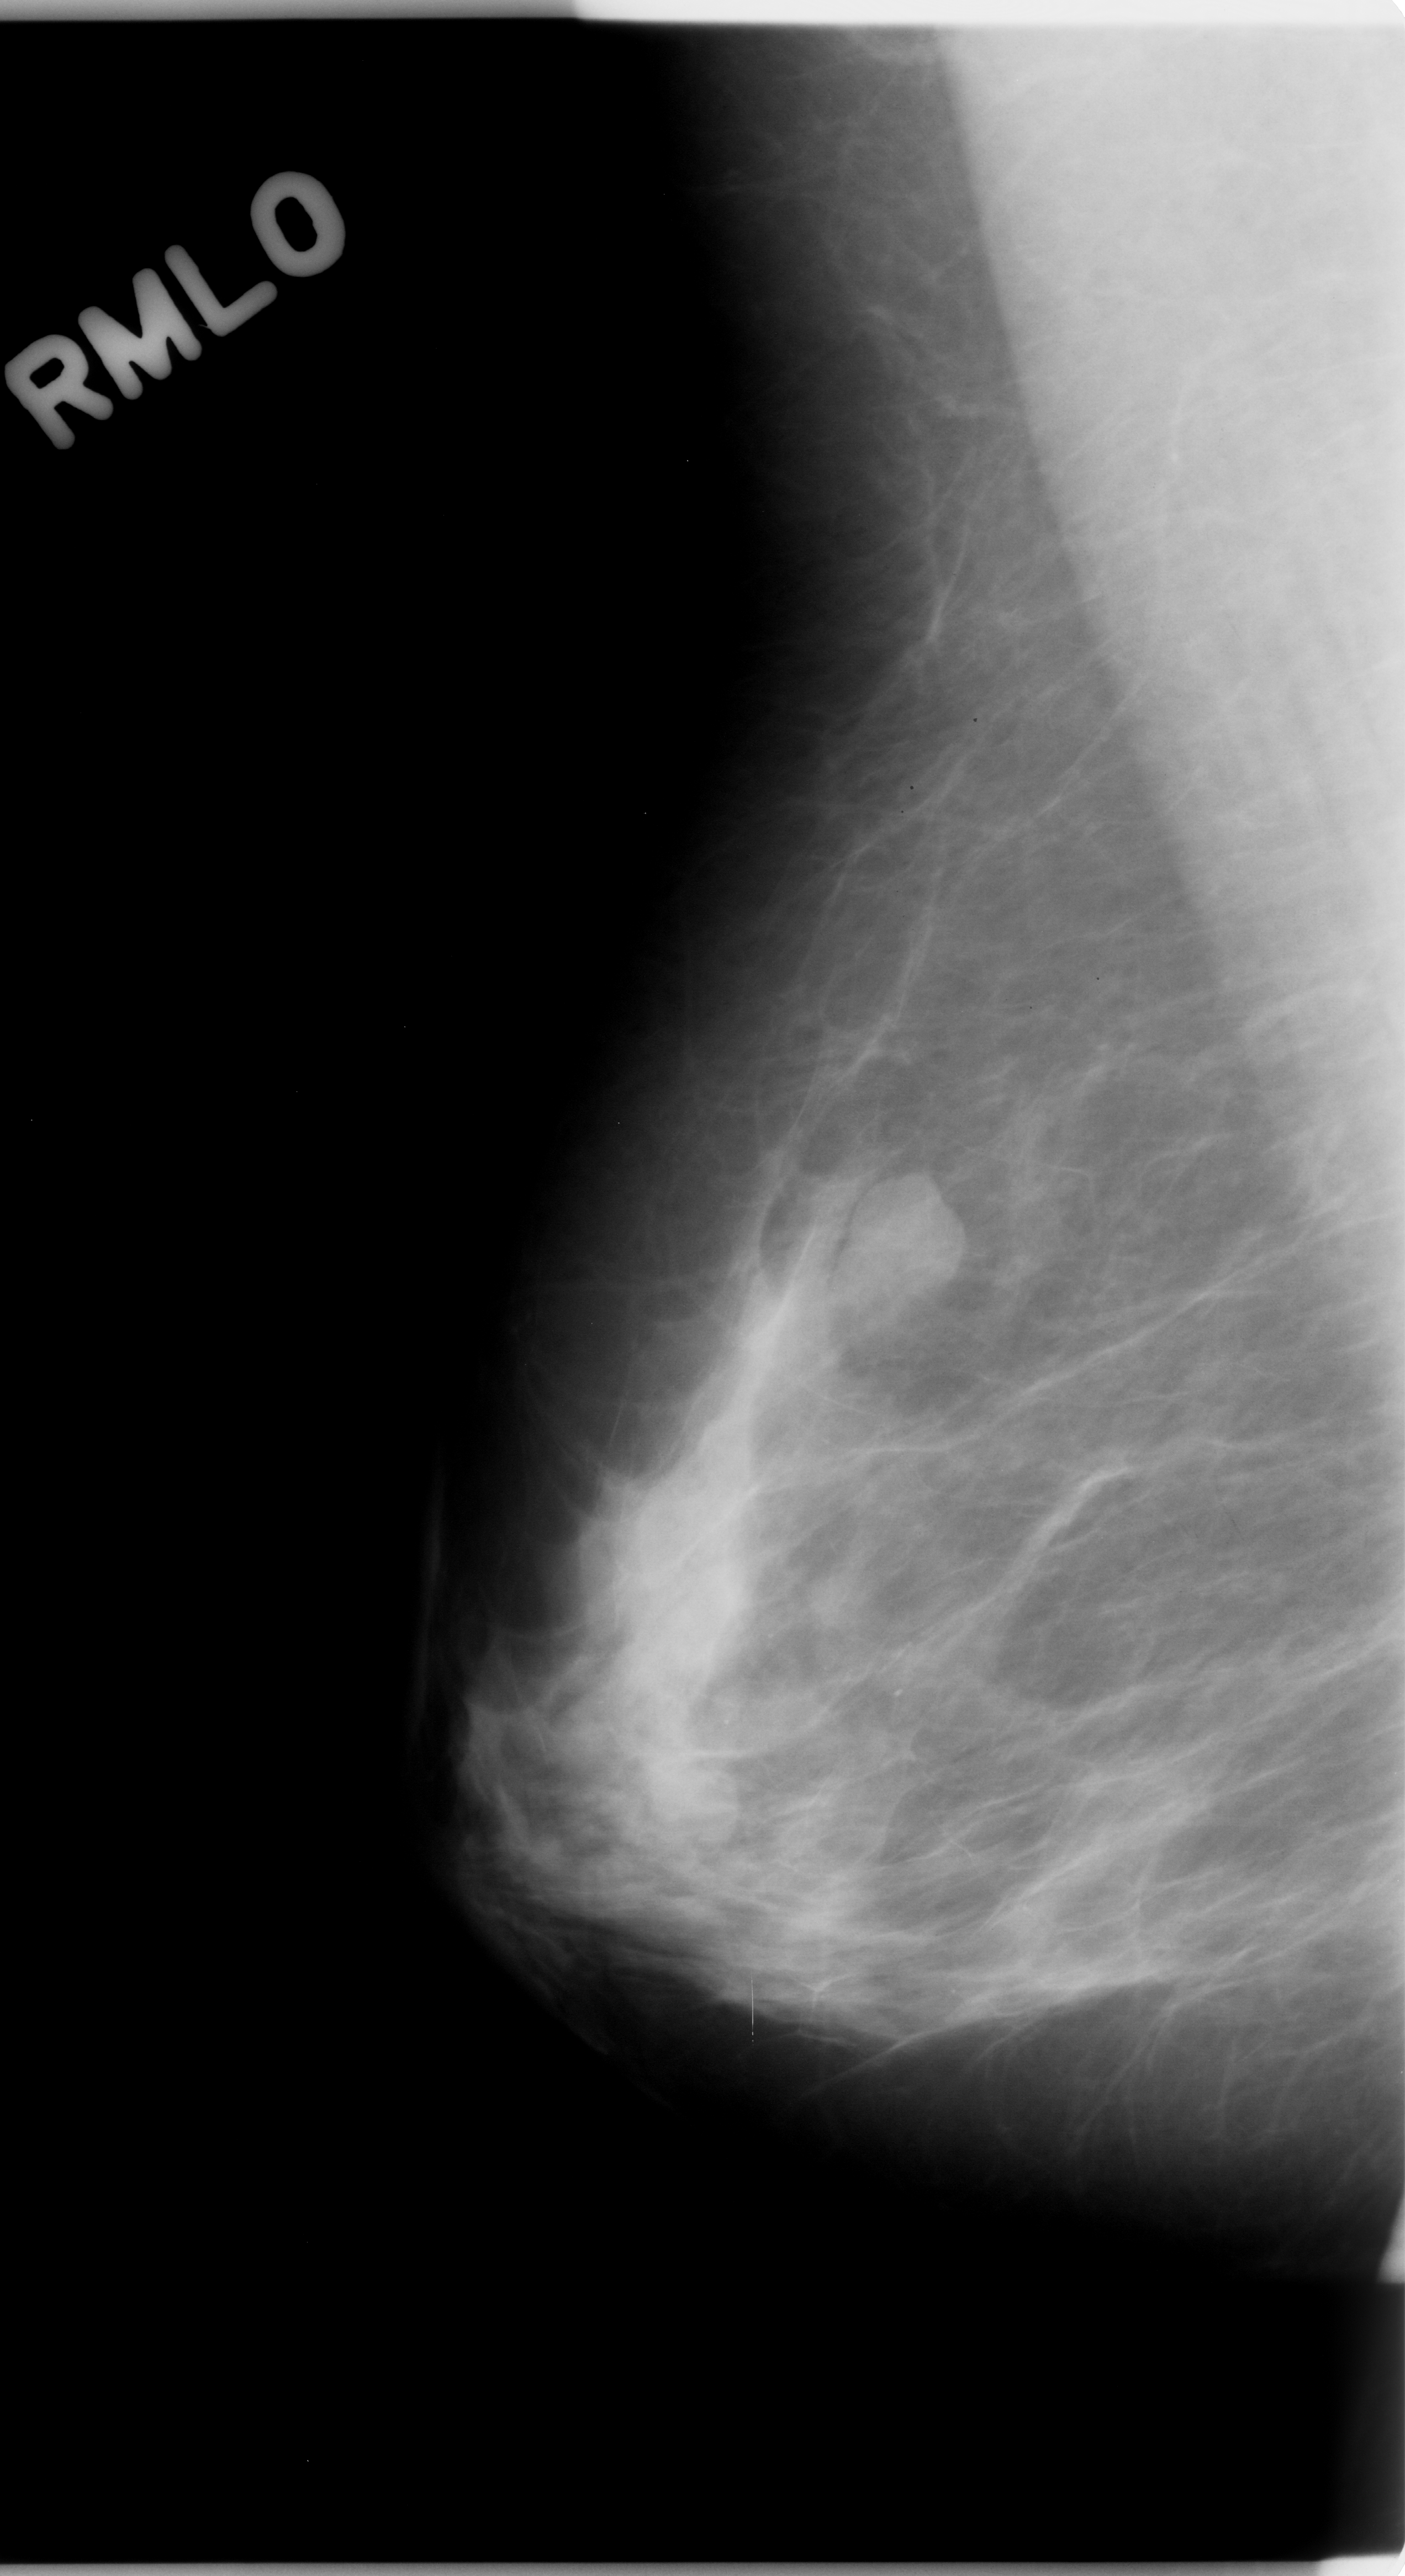
Scanned film-screen mammogram; right breast; mediolateral oblique (MLO) view; breast composition: scattered fibroglandular densities (BI-RADS density category 2 of 4).
Finding: mass, shape oval, margins circumscribed; BI-RADS assessment category 4; pathology (as recorded): benign.